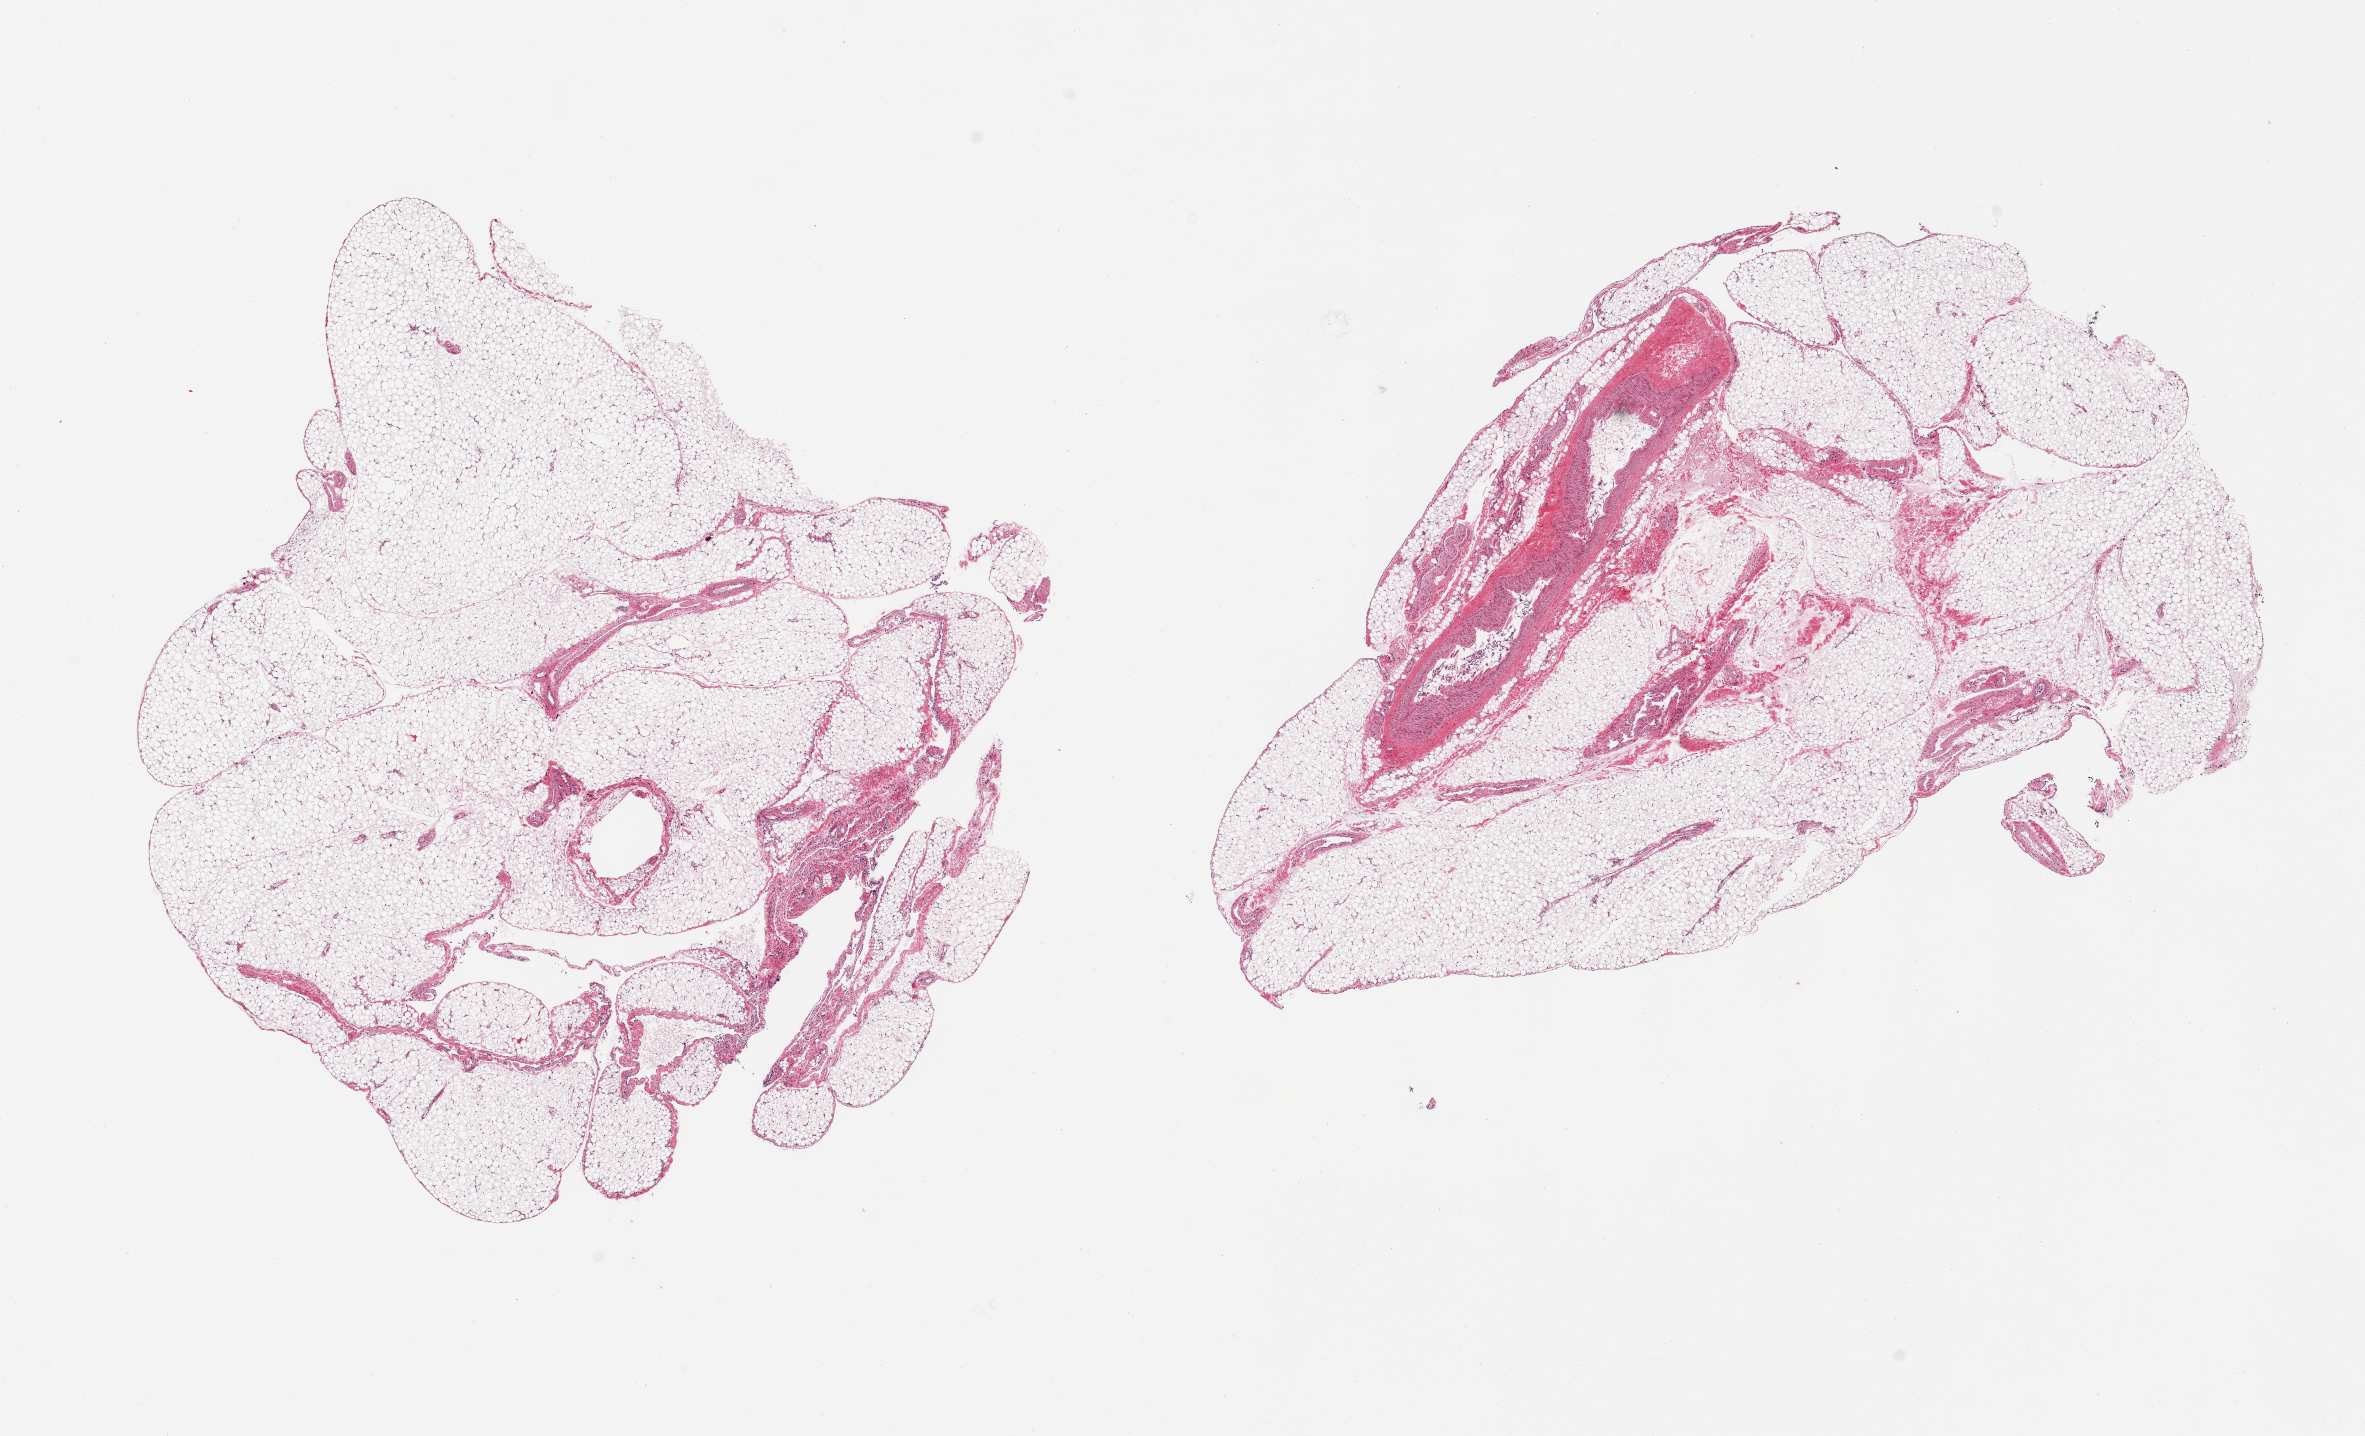
Digitized hematoxylin and eosin (H&E)-stained section, a low-resolution overview of the entire scanned area, about 18.7 x 11.4 mm (acquisition: 20x scan). PAXgene-fixed, paraffin-embedded tissue. Sampled site (target tissue): omentum. Donor tissue sample. Donor: female.
Pathologist's review note for this sample: 2 pieces, ~10-15% fascia/vascular elements.